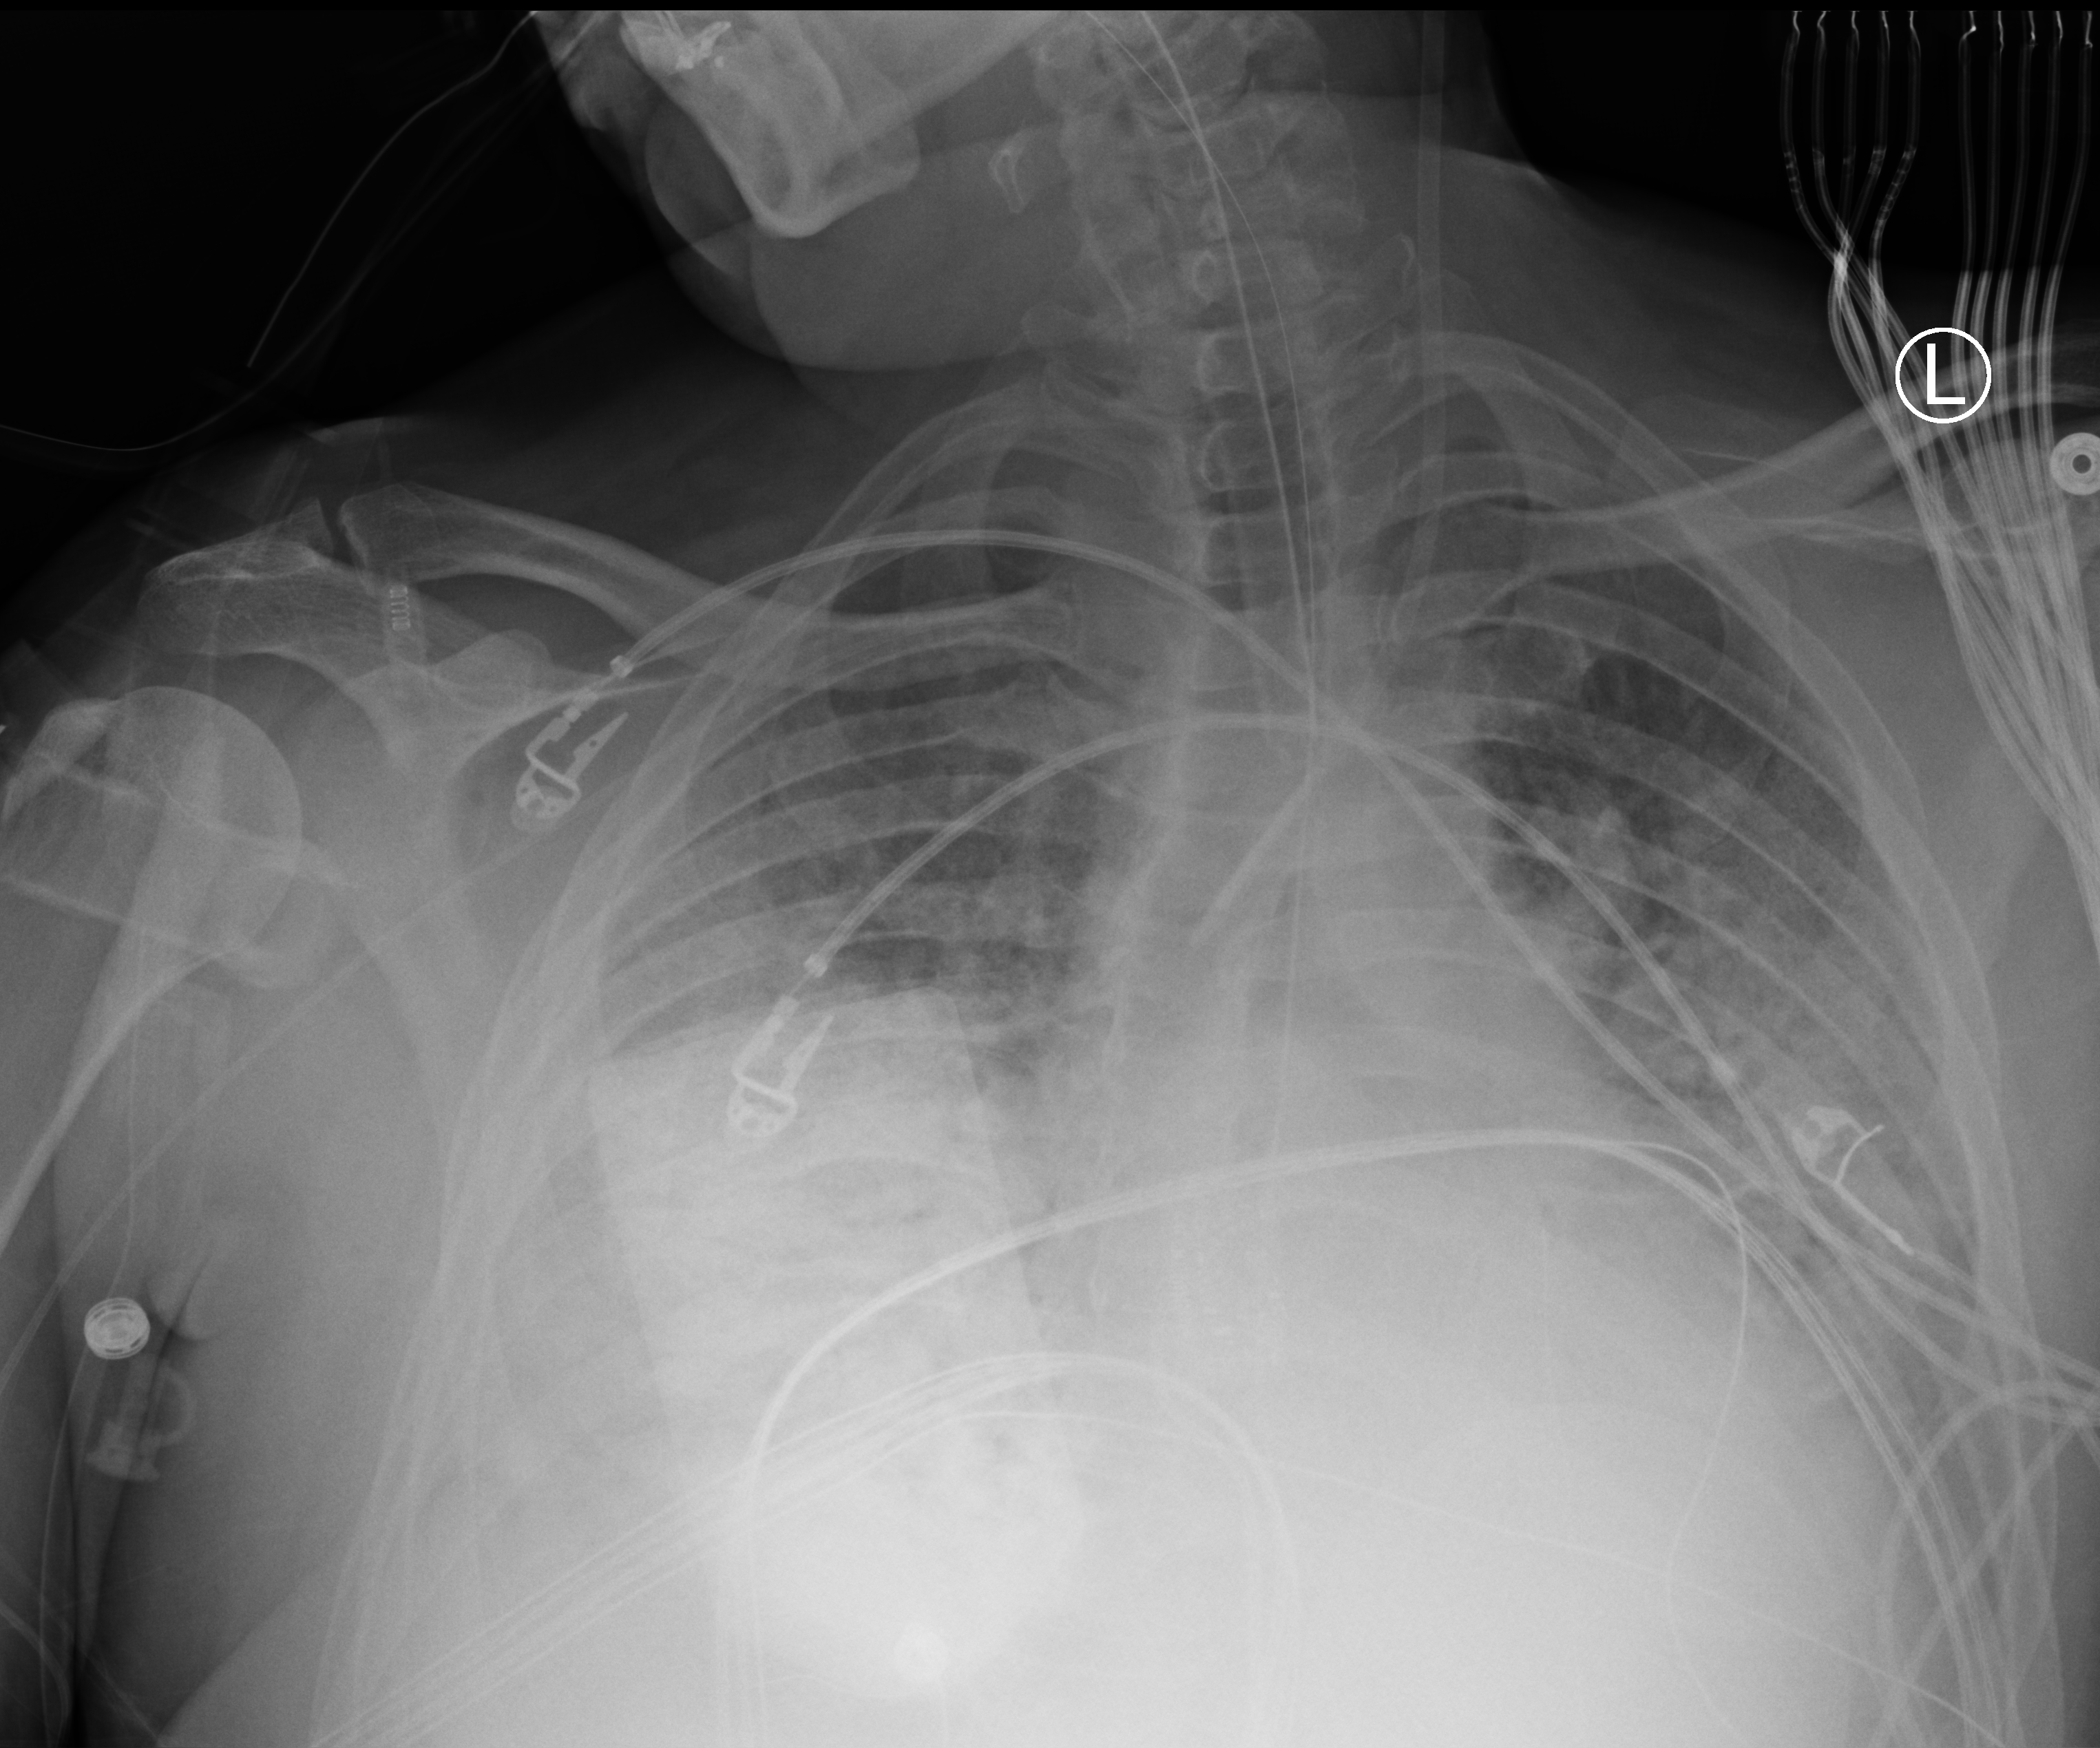
Portable chest radiograph, anteroposterior (AP) projection. Male patient hospitalised with COVID-19, age 18–59 years.
Hospital-stay facts (about this admission, not read from this image; timing relative to this image not recorded):
- mechanically ventilated during this hospital stay: yes
- admitted to intensive care during this hospital stay: yes